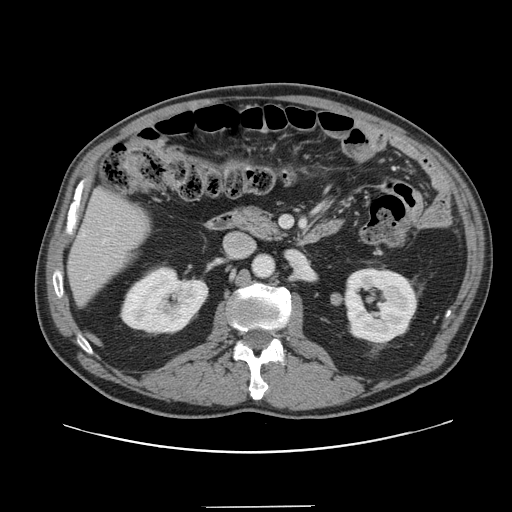
Contrast-enhanced abdominal CT, one axial slice; slice 61 of 139 in the series (ordered by position); 120 kVp; soft-tissue window (W 400 / L 40 HU); 512 × 512 image matrix, field of view 397 × 397 mm. Male patient, age 64 years. Case-level facts recorded for this patient, not image findings: diagnosis: colorectal cancer liver metastases, imaged before liver resection; multiple liver metastases: yes; largest metastasis: 3.5 cm; disease in both lobes: yes.
Structures marked on this image (manually delineated by an expert):
- liver: bounding box <69,192,149,302> (left, top, right, bottom; pixels)
- planned liver remnant (the part of the liver to remain after resection): <69,192,149,303>